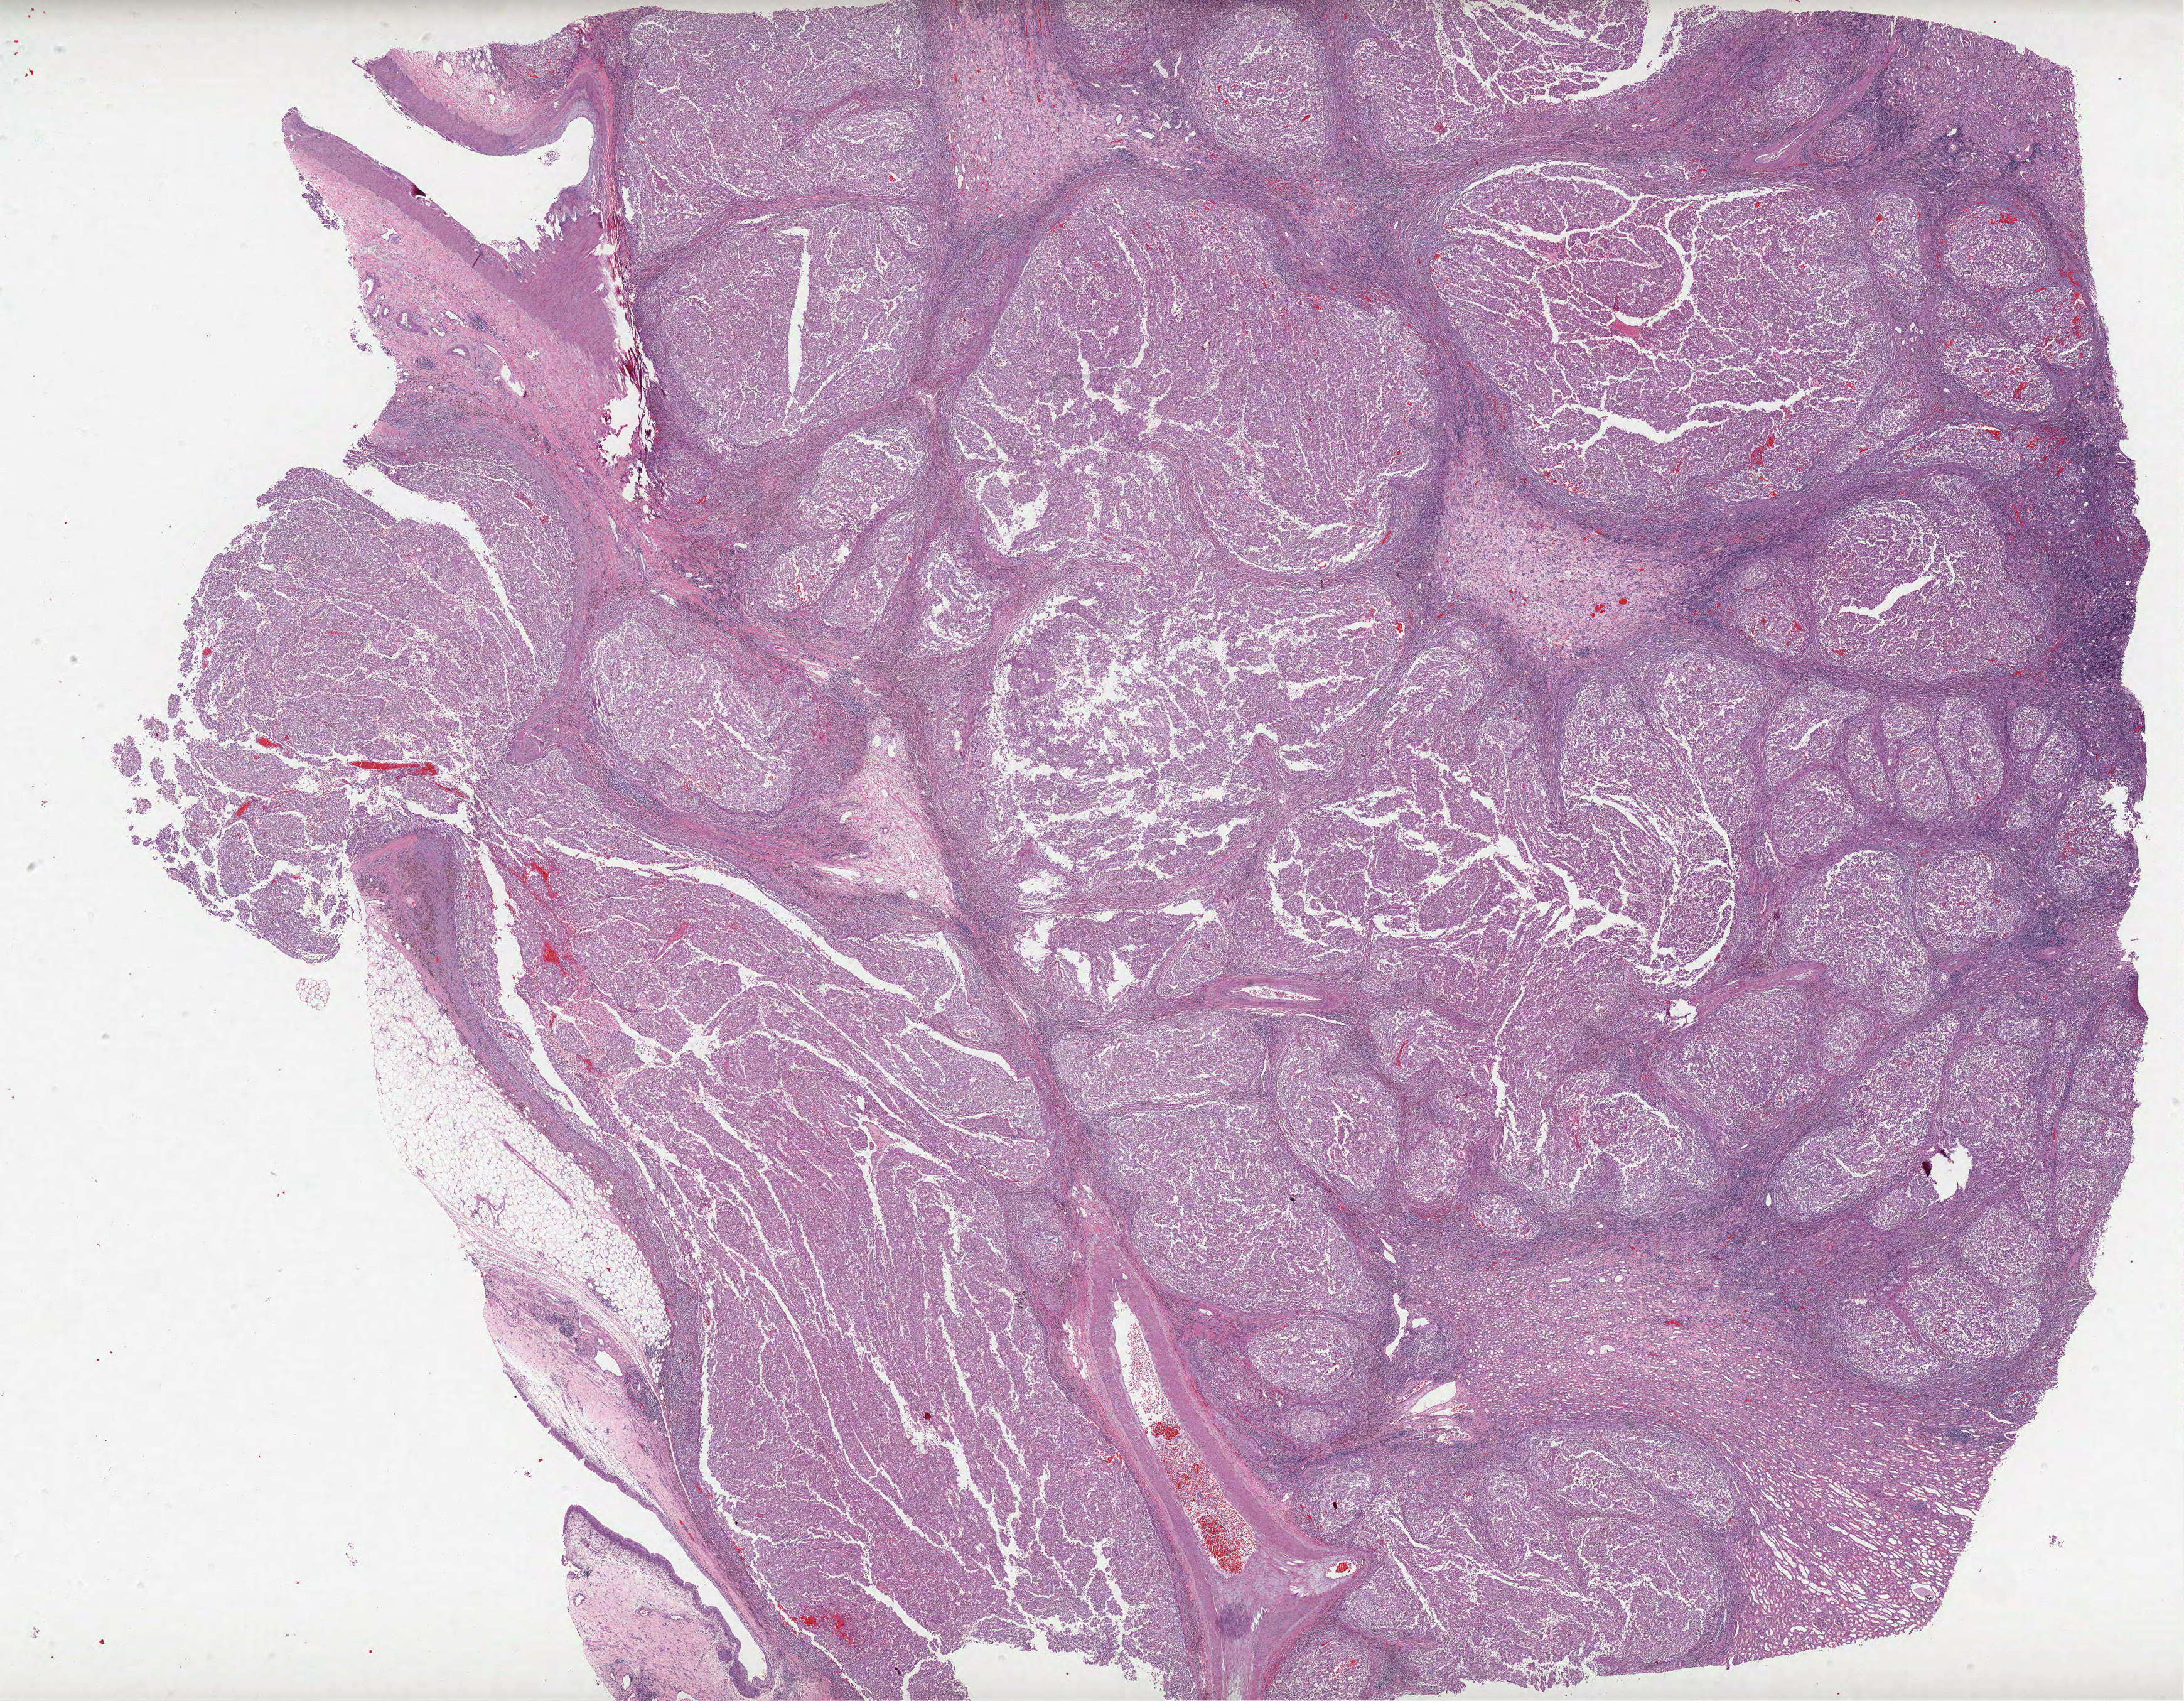
Hematoxylin and eosin (H&E) stained whole-slide image, whole scanned area (about 27.8 x 21.7 mm) shown as a low-resolution overview; formalin-fixed paraffin-embedded (FFPE) diagnostic section; primary tumour sample from the kidney. Patient: male, age at initial diagnosis 63 years.
AJCC pathologic stage: IV. Pathologic diagnosis: Papillary adenocarcinoma, NOS. TNM: T3b N1 M1.